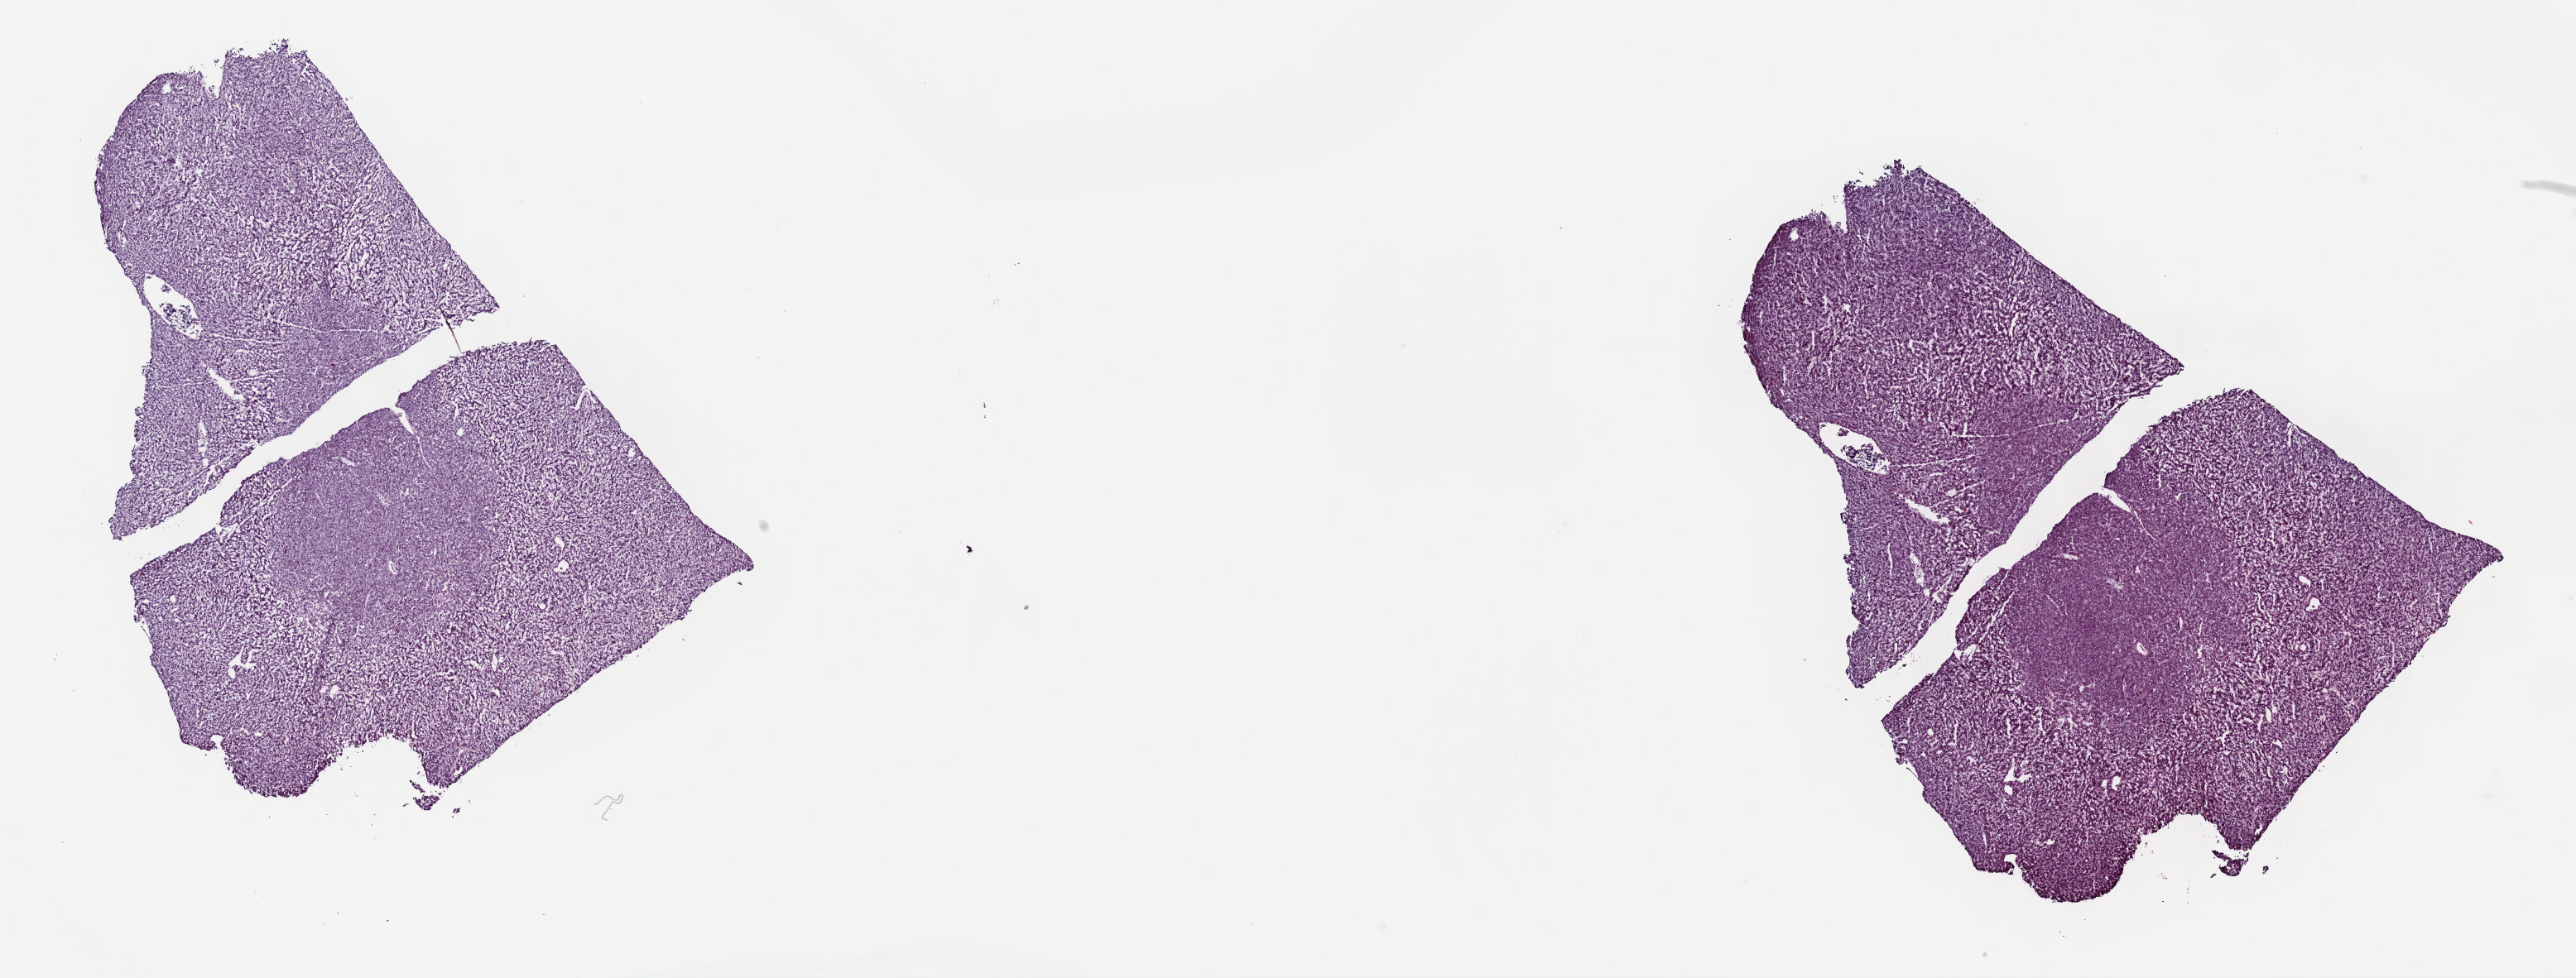
Whole-slide histology image, H&E — shown as a low-resolution overview of the whole scanned area (about 25.2 x 9.6 mm); frozen section; primary tumour sample from the liver. Male, age 65 years at initial diagnosis. Histologic grade: G1 (well differentiated). Pathologist review of this section (percent, as recorded): tumour cells 96%, tumour nuclei 95%, normal cells 0%, stromal cells 3%, necrosis 1%. Inflammatory infiltration, as recorded: lymphocyte infiltration 4%, monocyte infiltration 0%, neutrophil infiltration 0%.
- AJCC pathologic stage: IIIB (7th edition)
- diagnosis: Hepatocellular carcinoma, NOS